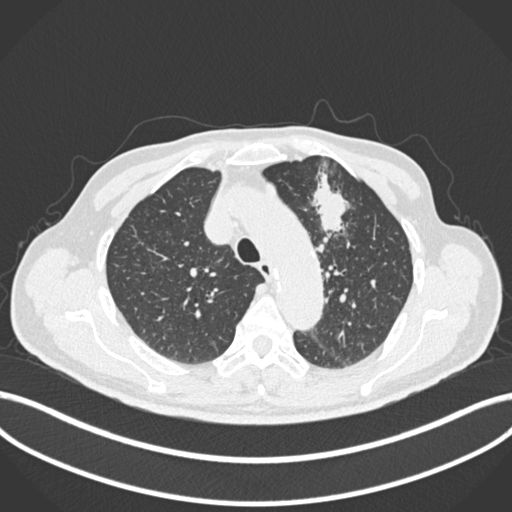
Chest CT, one axial slice; position 189 of 261 along the scan axis; reconstruction kernel B30f; 120 kVp; lung window (W 1500 / L -600 HU); 512 × 512 image matrix, field of view 400 × 400 mm. Patient: male, 74 years. From the clinical record (not read from this slice): clinical TNM (as recorded): T2b N0 M1c.
Annotated regions visible in this slice (rectangle marked by the reading radiologist):
- lung tumour (recorded histology: adenocarcinoma): box from (x=311, y=173) to (x=358, y=245) px